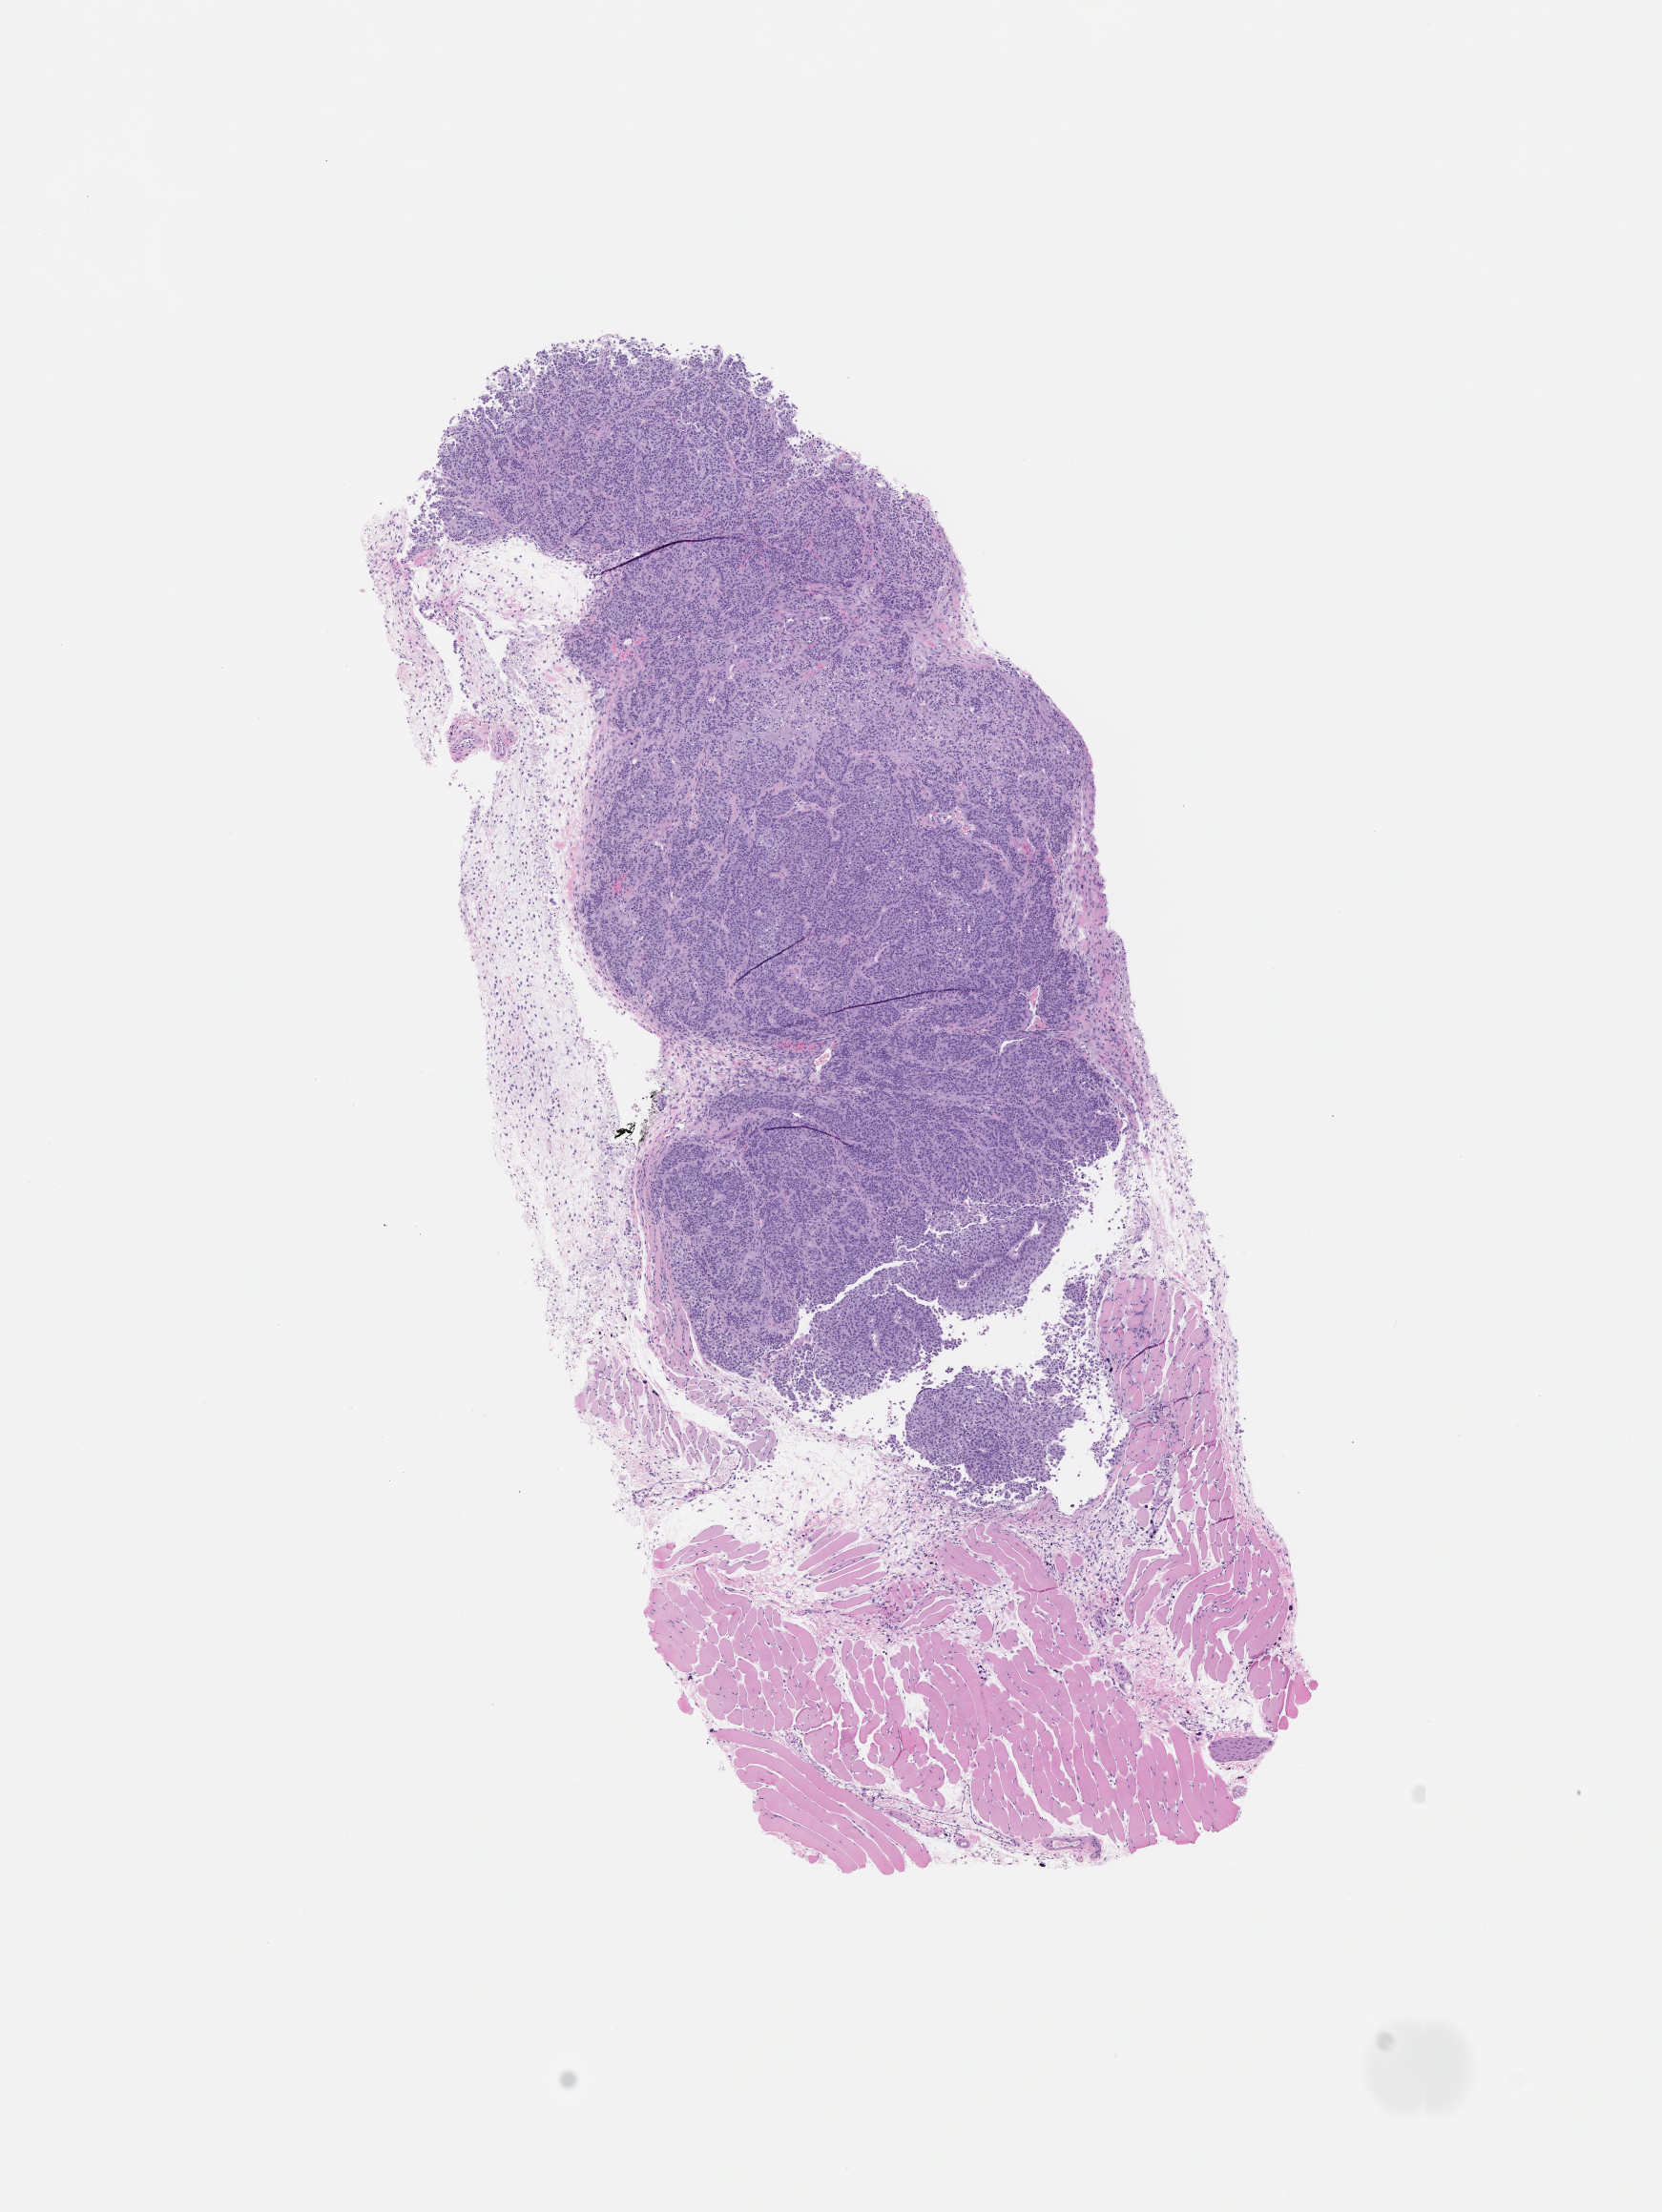
Whole-slide image, H&E: patient-derived xenograft (human tumor grown in a mouse), passage 1, whole scanned area (about 7.0 x 9.3 mm) shown as a low-resolution overview; FFPE section; tumor site category: bladder.
Originating patient diagnosis: Urothelial Carcinoma.